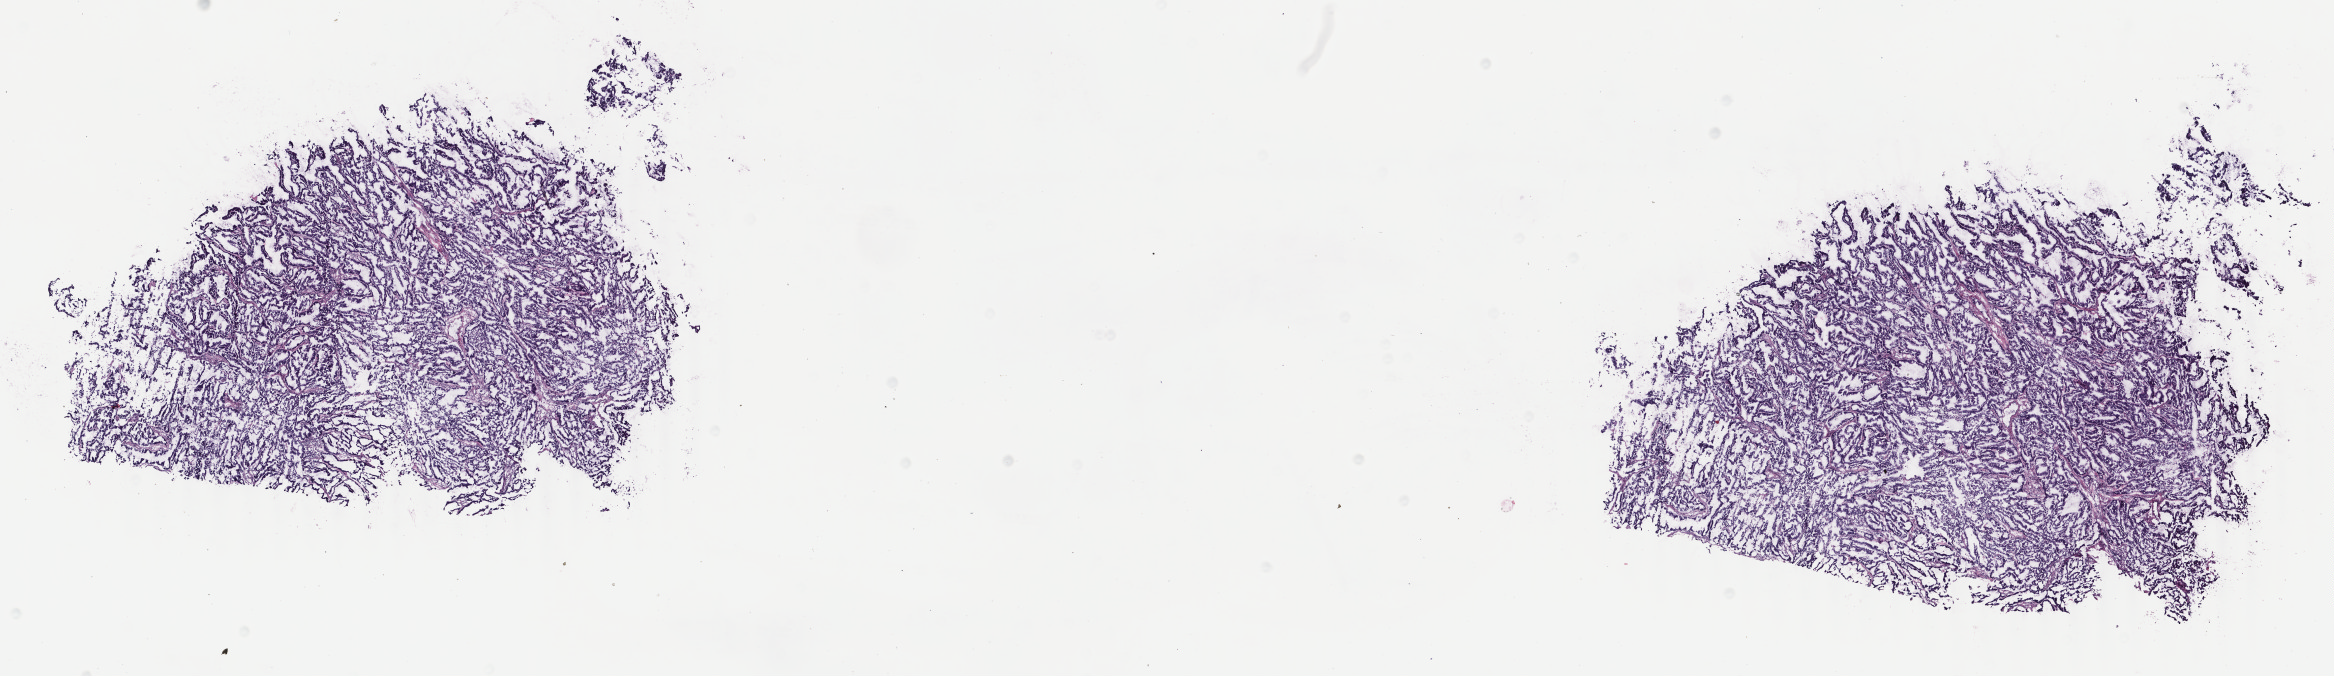
H&E-stained whole-slide image, low-resolution overview of the scanned area, about 18.6 x 5.4 mm, frozen section, primary tumour sample from the uterus. Female, age 56 years at initial diagnosis. Slide review estimates, as recorded: tumour cells 100%, tumour nuclei 90%.
Histologic diagnosis: Endometrioid adenocarcinoma, NOS (endometrium).